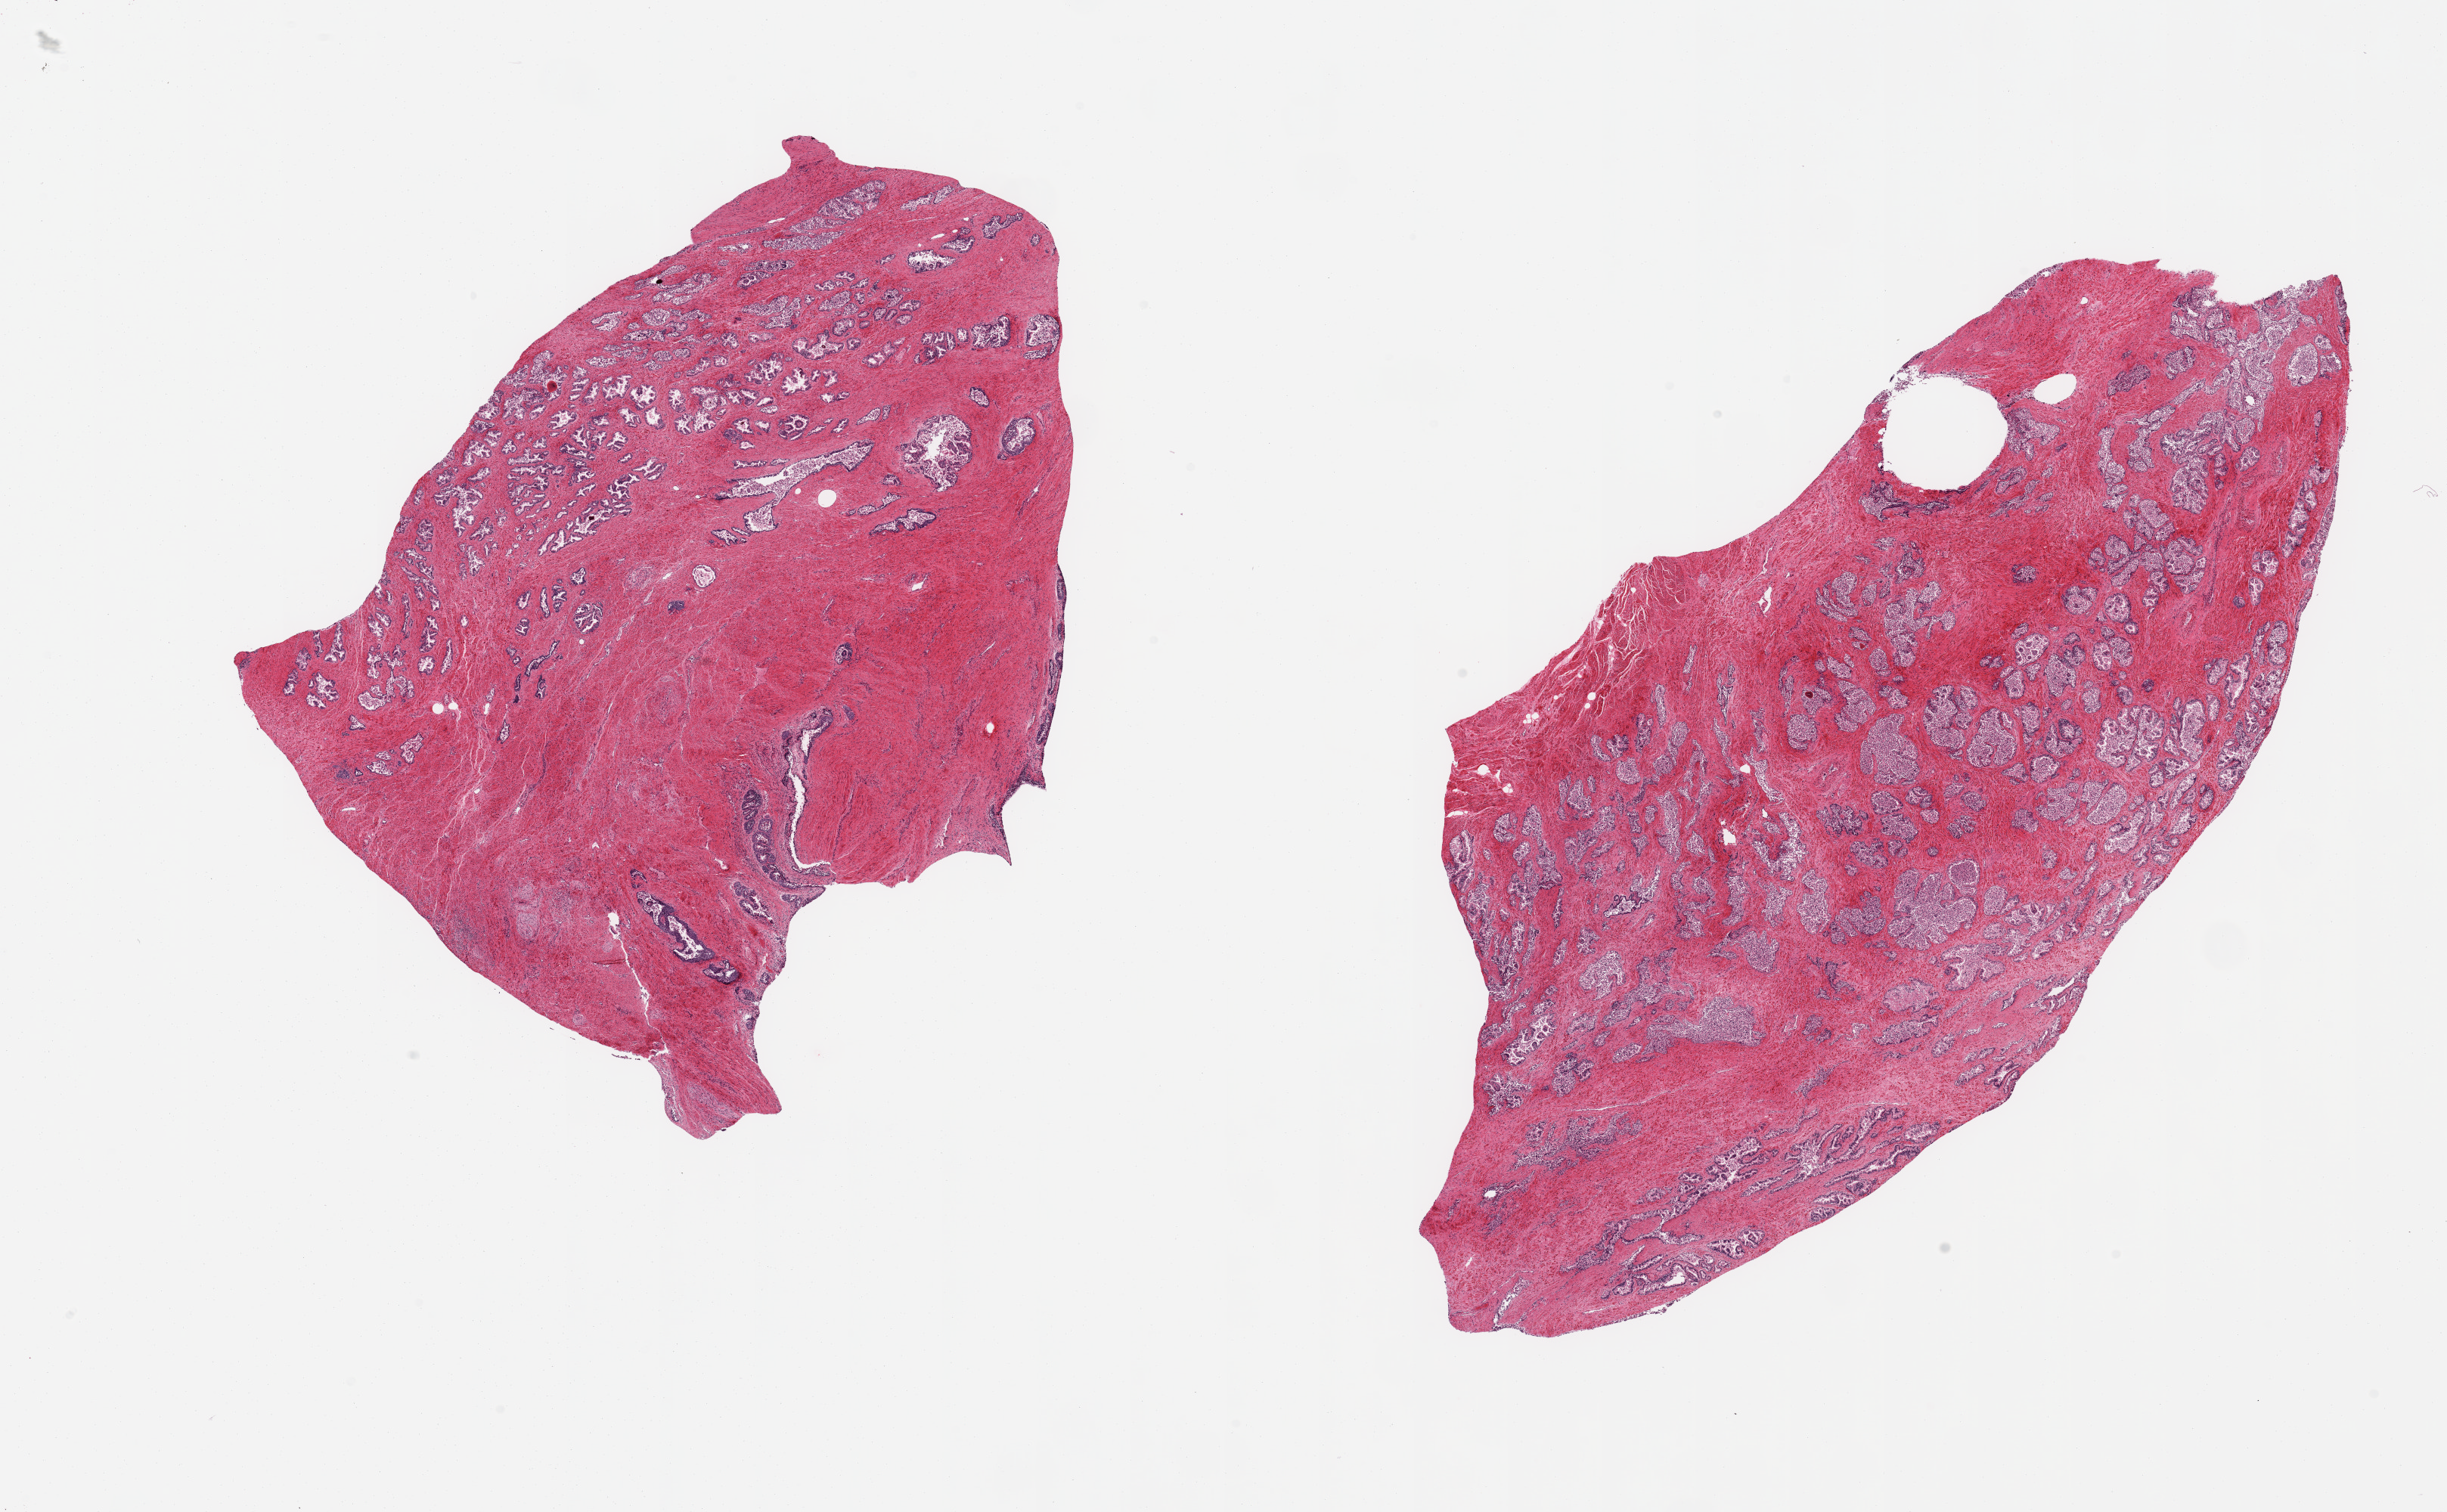
Hematoxylin and eosin (H&E) whole-slide image, whole scanned area (about 25.6 x 15.8 mm) shown as a low-resolution overview, PAXgene-fixed, paraffin-embedded tissue, section of prostate (target tissue), donor tissue sample. Donor: male.
Review note (as recorded): 2 pieces, 1 with well preserved acini and periurethral ducts; the other has severely autolyzed glands and intact stroma.